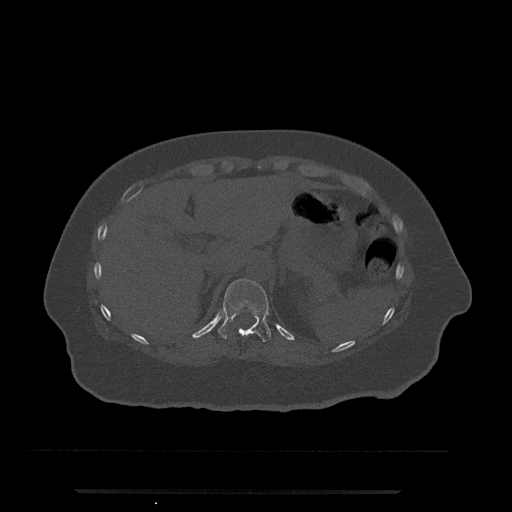
CT including the spine, one axial slice; slice 232 of 797 in the series (ordered by position); reconstruction kernel Br40s/3; 120 kVp; bone window (W 1800 / L 400 HU); 0.5 mm slice thickness; 512 × 512 image matrix, field of view 440 × 440 mm. Patient: female, 51 years. Case-level facts recorded for this patient, not image findings: primary cancer: neuro; vertebrae with lytic lesions (as recorded): T8.
Annotated regions visible in this slice (semi-automatically segmented with operator editing):
- T11 vertebra: bounding box [x1, y1, x2, y2] px = [218, 279, 271, 342]